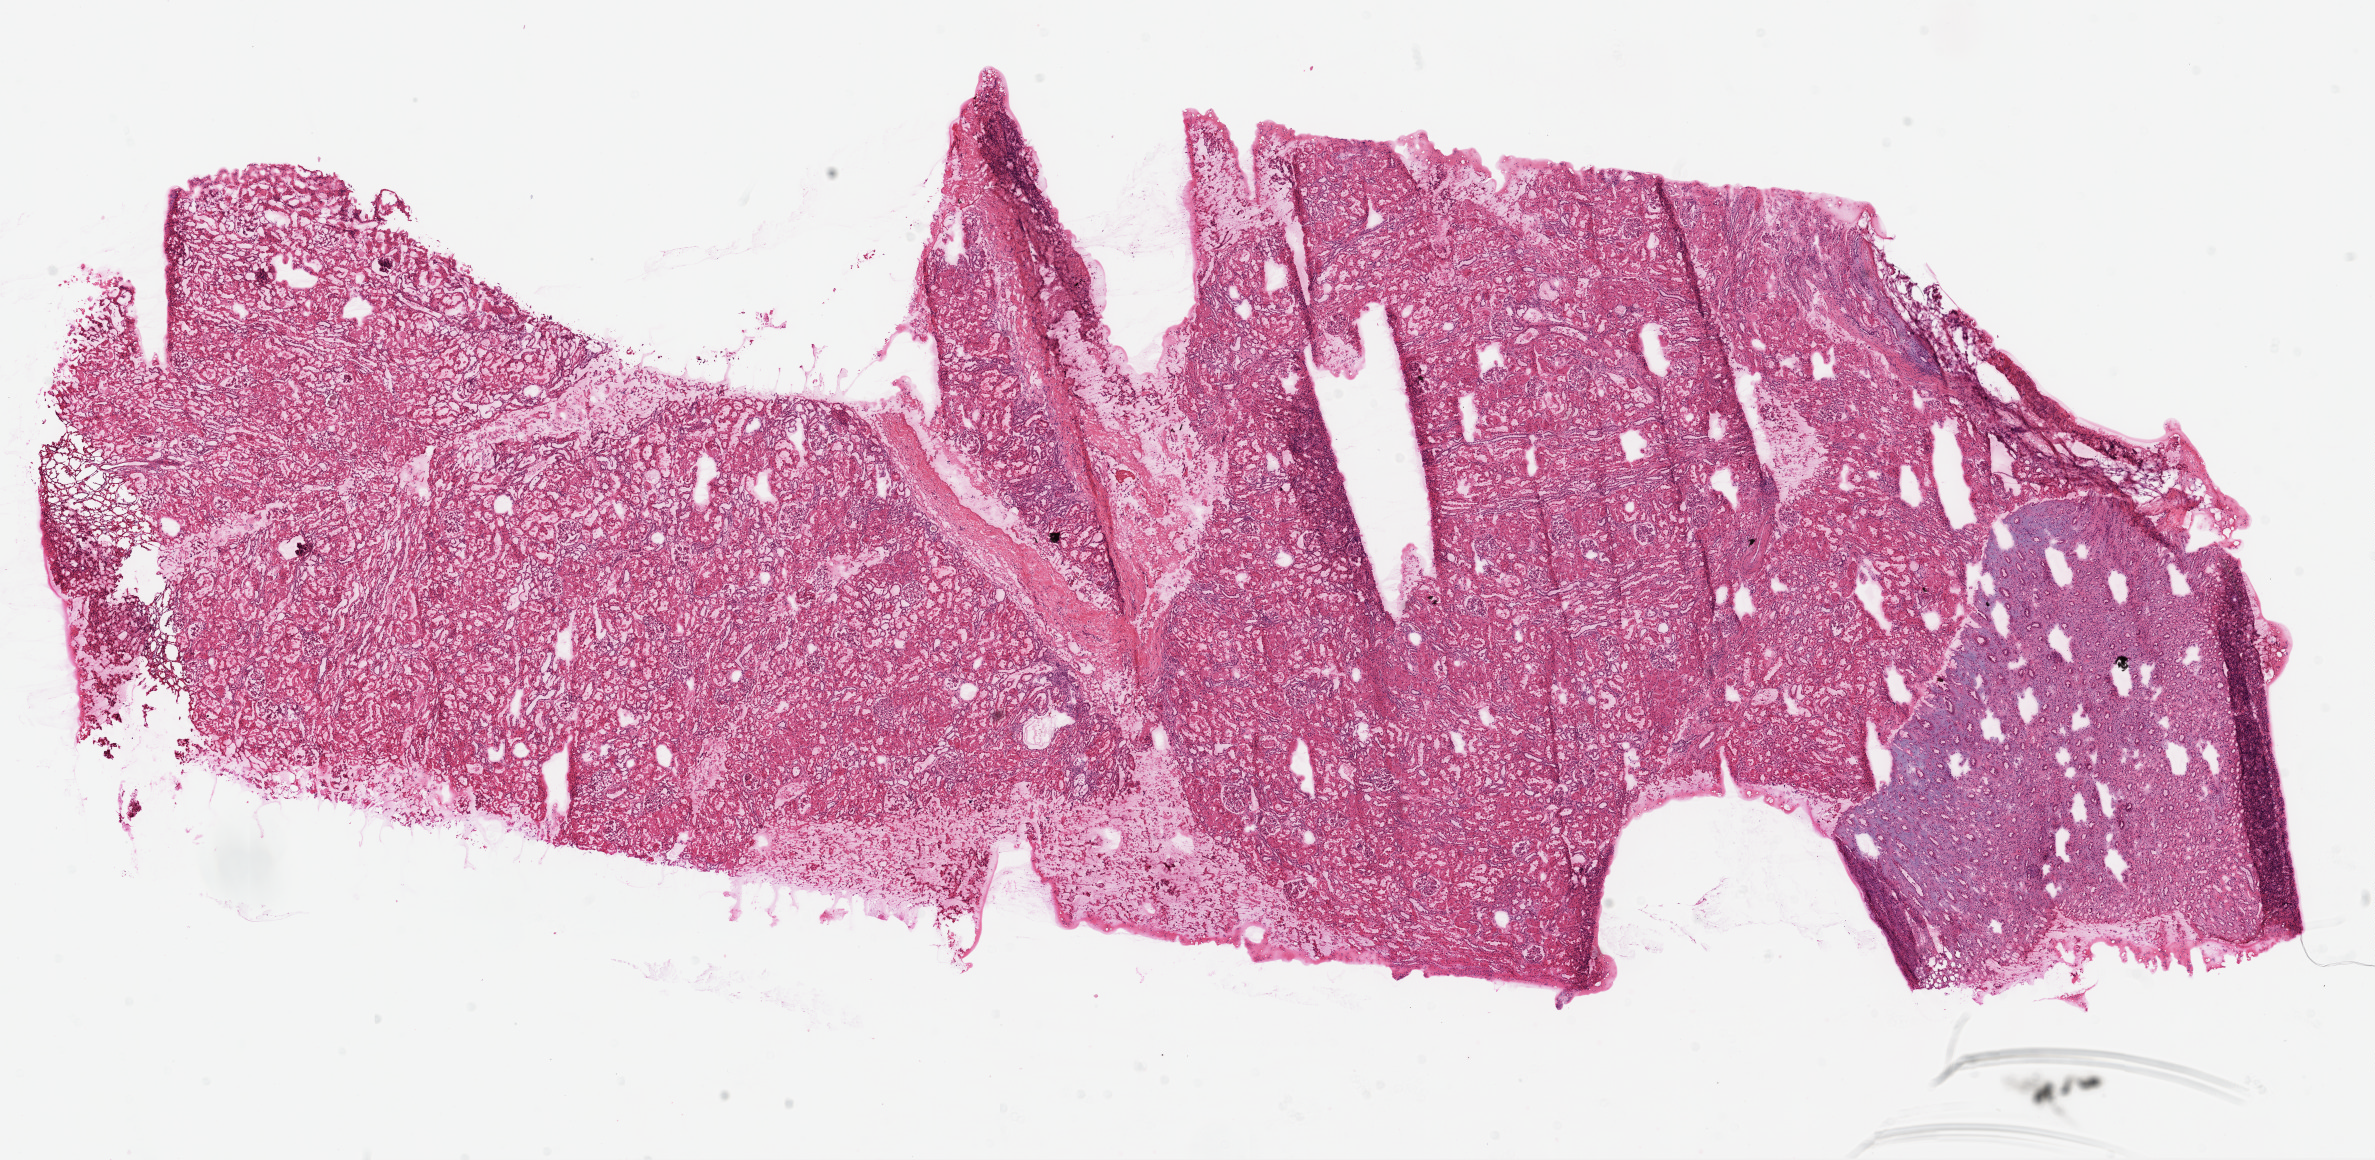
Whole-slide histology image, Hematoxylin and eosin (H&E) stained, low-resolution overview of the scanned area, about 19.1 x 9.3 mm (slide scanned at 20x); frozen section from the top of the tissue portion; sample: solid tissue normal (non-tumour tissue), kidney. Patient: female, age at initial diagnosis 48 years.
• this section: solid tissue normal (non-tumour) sample from the same patient
• patient diagnosis: Clear cell adenocarcinoma, NOS